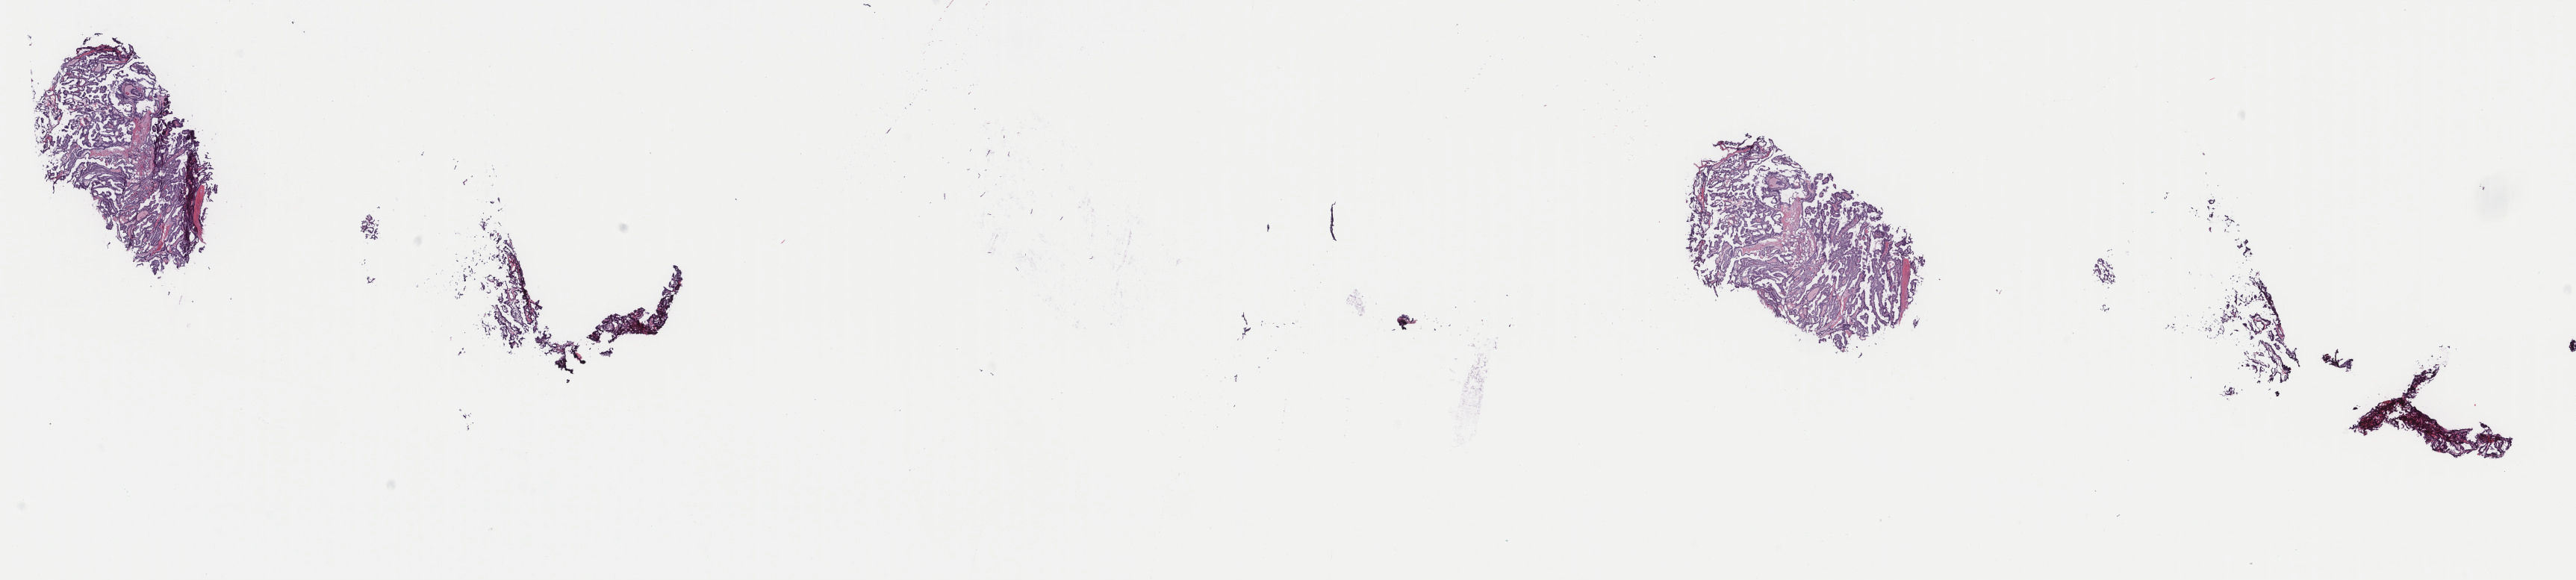
H&E whole-slide image, low-resolution overview of the scanned area, about 27.4 x 6.2 mm (from a 40x scan). Frozen section. Thyroid, primary tumour sample. Patient: female, age at initial diagnosis 42 years. Pathologist review of this section (percent, as recorded): tumour cells 90%, tumour nuclei 75%, normal cells 0%, stromal cells 10%, necrosis 0%. Infiltration values recorded for this section: lymphocyte infiltration 4%, monocyte infiltration 1%, neutrophil infiltration 0%.
AJCC pathologic stage: I (7th edition). Lymph nodes positive (case pathology): 17 of 55 examined. Laterality: right. Pathologic diagnosis: Papillary carcinoma, follicular variant (thyroid gland).